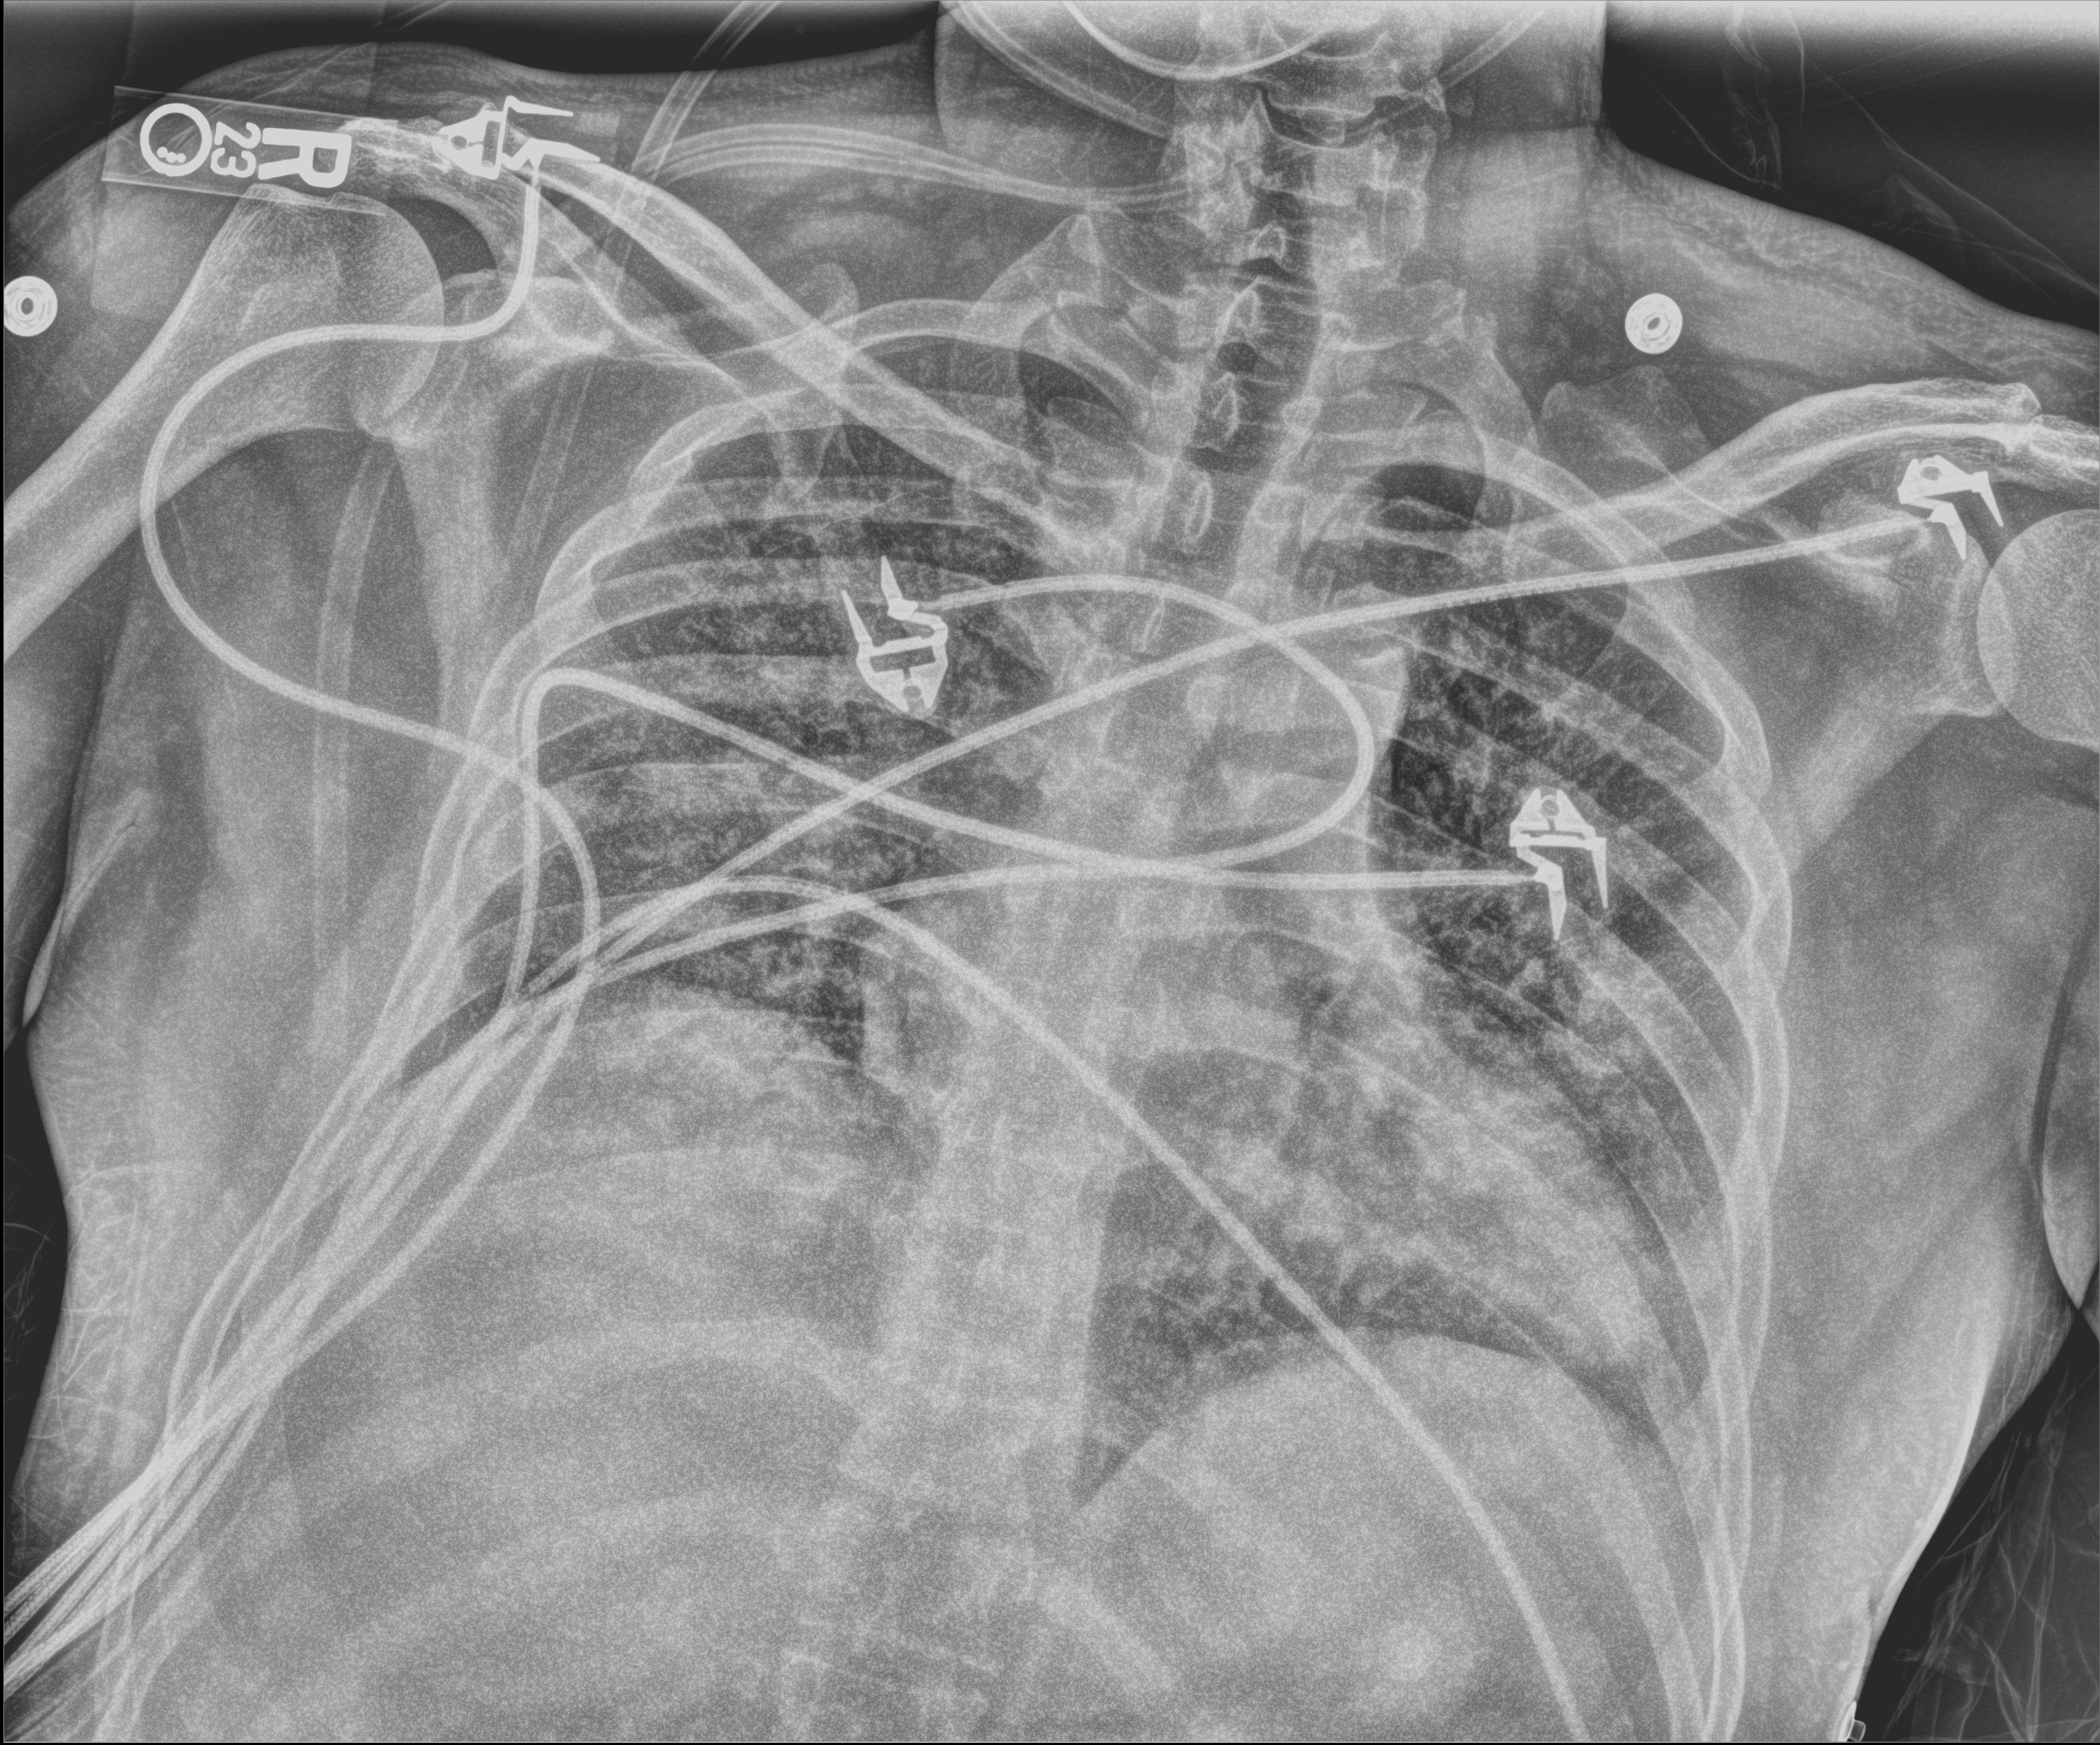
Portable chest radiograph; anteroposterior (AP) projection. Patient hospitalised with COVID-19; male, aged 18–59 years.
Hospital-stay facts (about this admission, not read from this image; timing relative to this image not recorded):
- chronic kidney disease (admission record): no